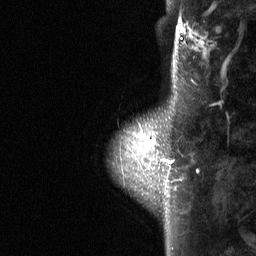
Breast MRI (dynamic contrast-enhanced), one sagittal slice. Position 13 of 64 along the scan axis. Dynamic contrast-enhanced study with each time point stored as its own series, time point 2 of 3 at this slice position (early post-contrast, ordered by acquisition time). 1.5 T. TE 4.8 ms, TR 27 ms. 256 × 256 image matrix. Female patient, age 42 years. Case-level facts recorded for this patient, not image findings: setting: breast cancer imaged before/during neoadjuvant chemotherapy; receptor status: triple-negative.
Outlined on this slice (semi-automatic segmentation, software-assisted and operator-edited):
- analysis volume of interest (the breast-tissue region the enhancement analysis was run in; not a lesion): bounding box <112,104,187,178> (left, top, right, bottom; pixels)
- tumour enhancement mask (voxels above the 90 % enhancement threshold inside the analysis volume of interest): <151,141,173,163>